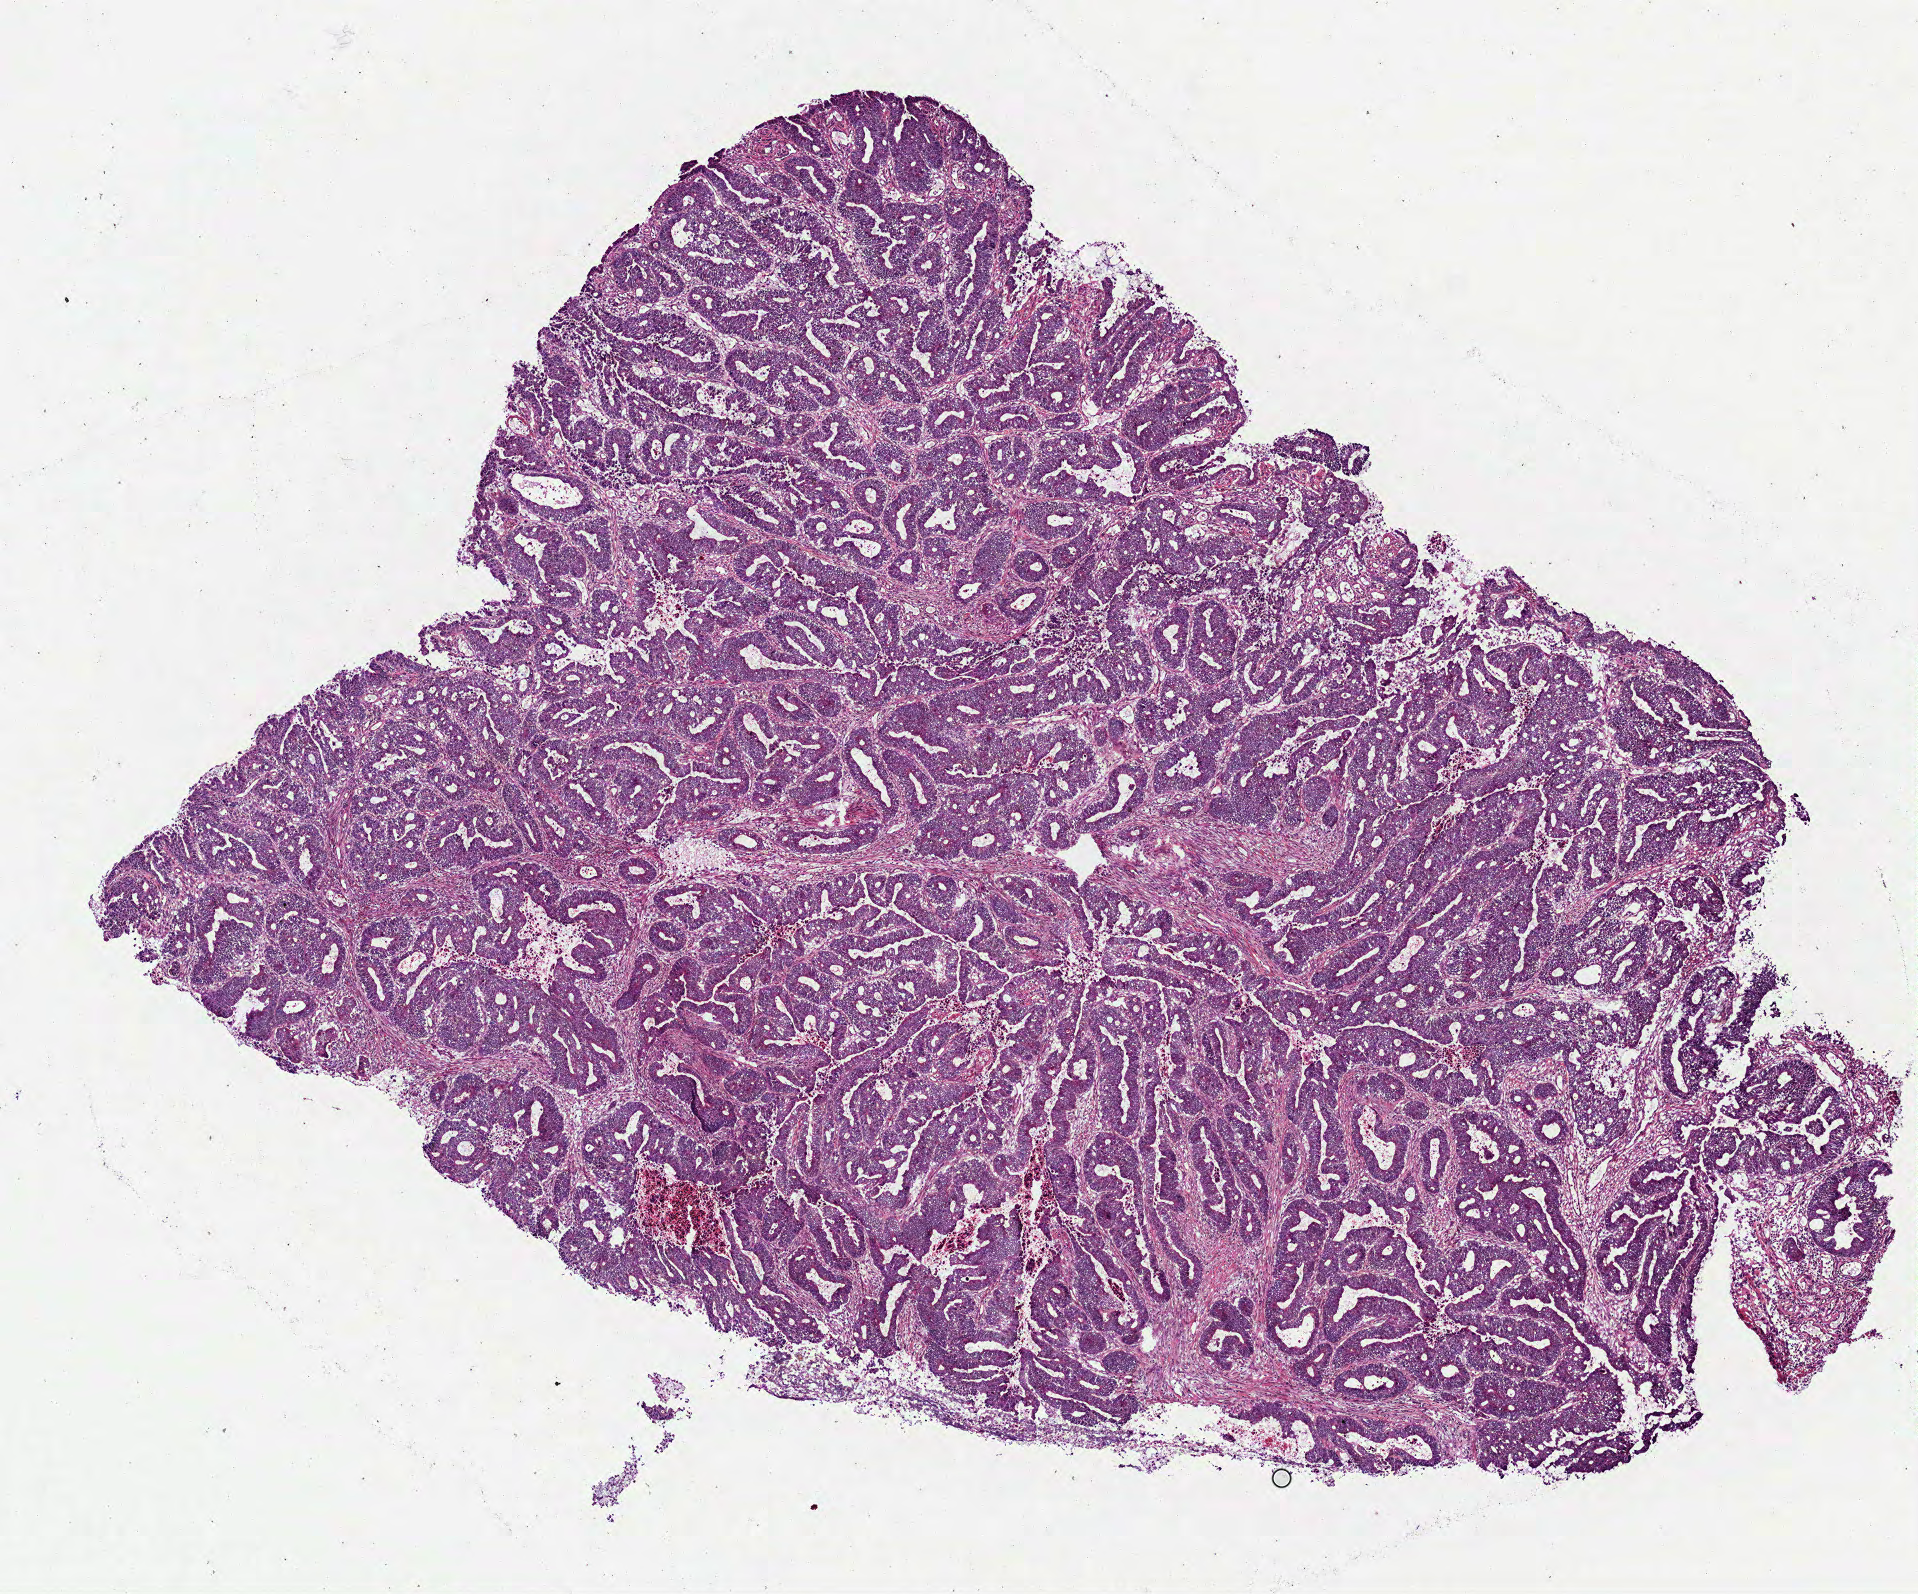
Digitized Hematoxylin and eosin (H&E) stained tissue section (whole slide), a low-resolution overview of the entire scanned area, about 7.7 x 6.4 mm (from a 40x scan), frozen section from the bottom of the tissue portion, colon, primary tumour sample. Male, age 81 years at initial diagnosis. Pathologist review of this section (percent, as recorded): tumour cells 85%, tumour nuclei 80%, normal cells 0%, stromal cells 10%, necrosis 5%.
TNM: T3 N1 MX. Histologic diagnosis: Adenocarcinoma, NOS. AJCC pathologic stage: IIIB (6th edition).